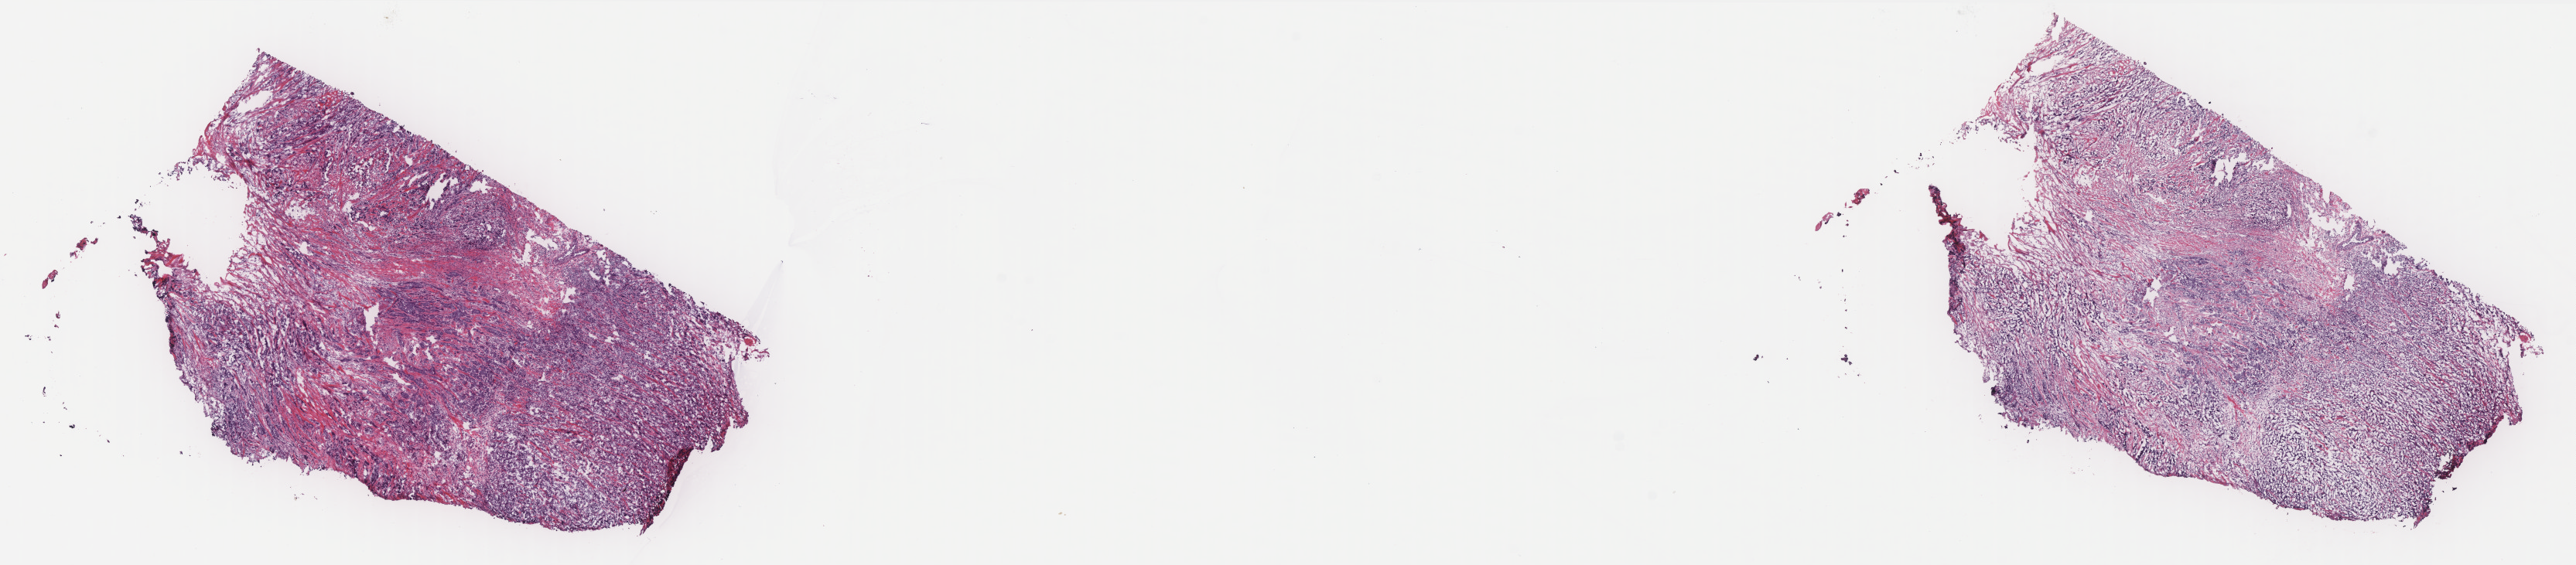
Digitized Hematoxylin and eosin (H&E) stained tissue section (whole slide), whole scanned area (about 26.7 x 5.9 mm) shown as a low-resolution overview. Frozen section from the bottom of the tissue portion. Breast, primary tumour sample. Female, age 68 years at initial diagnosis. Slide review estimates, as recorded: tumour cells 70%, tumour nuclei 80%, normal cells 30%, stromal cells 0%, necrosis 0%. Inflammatory infiltration, as recorded: lymphocyte infiltration 0%, monocyte infiltration 0%, neutrophil infiltration 0%.
AJCC pathologic stage: IIIA. Pathologic diagnosis: Infiltrating duct carcinoma, NOS. TNM: T2 N2 M0. Lymph nodes positive (case pathology): 1 of 15 examined.